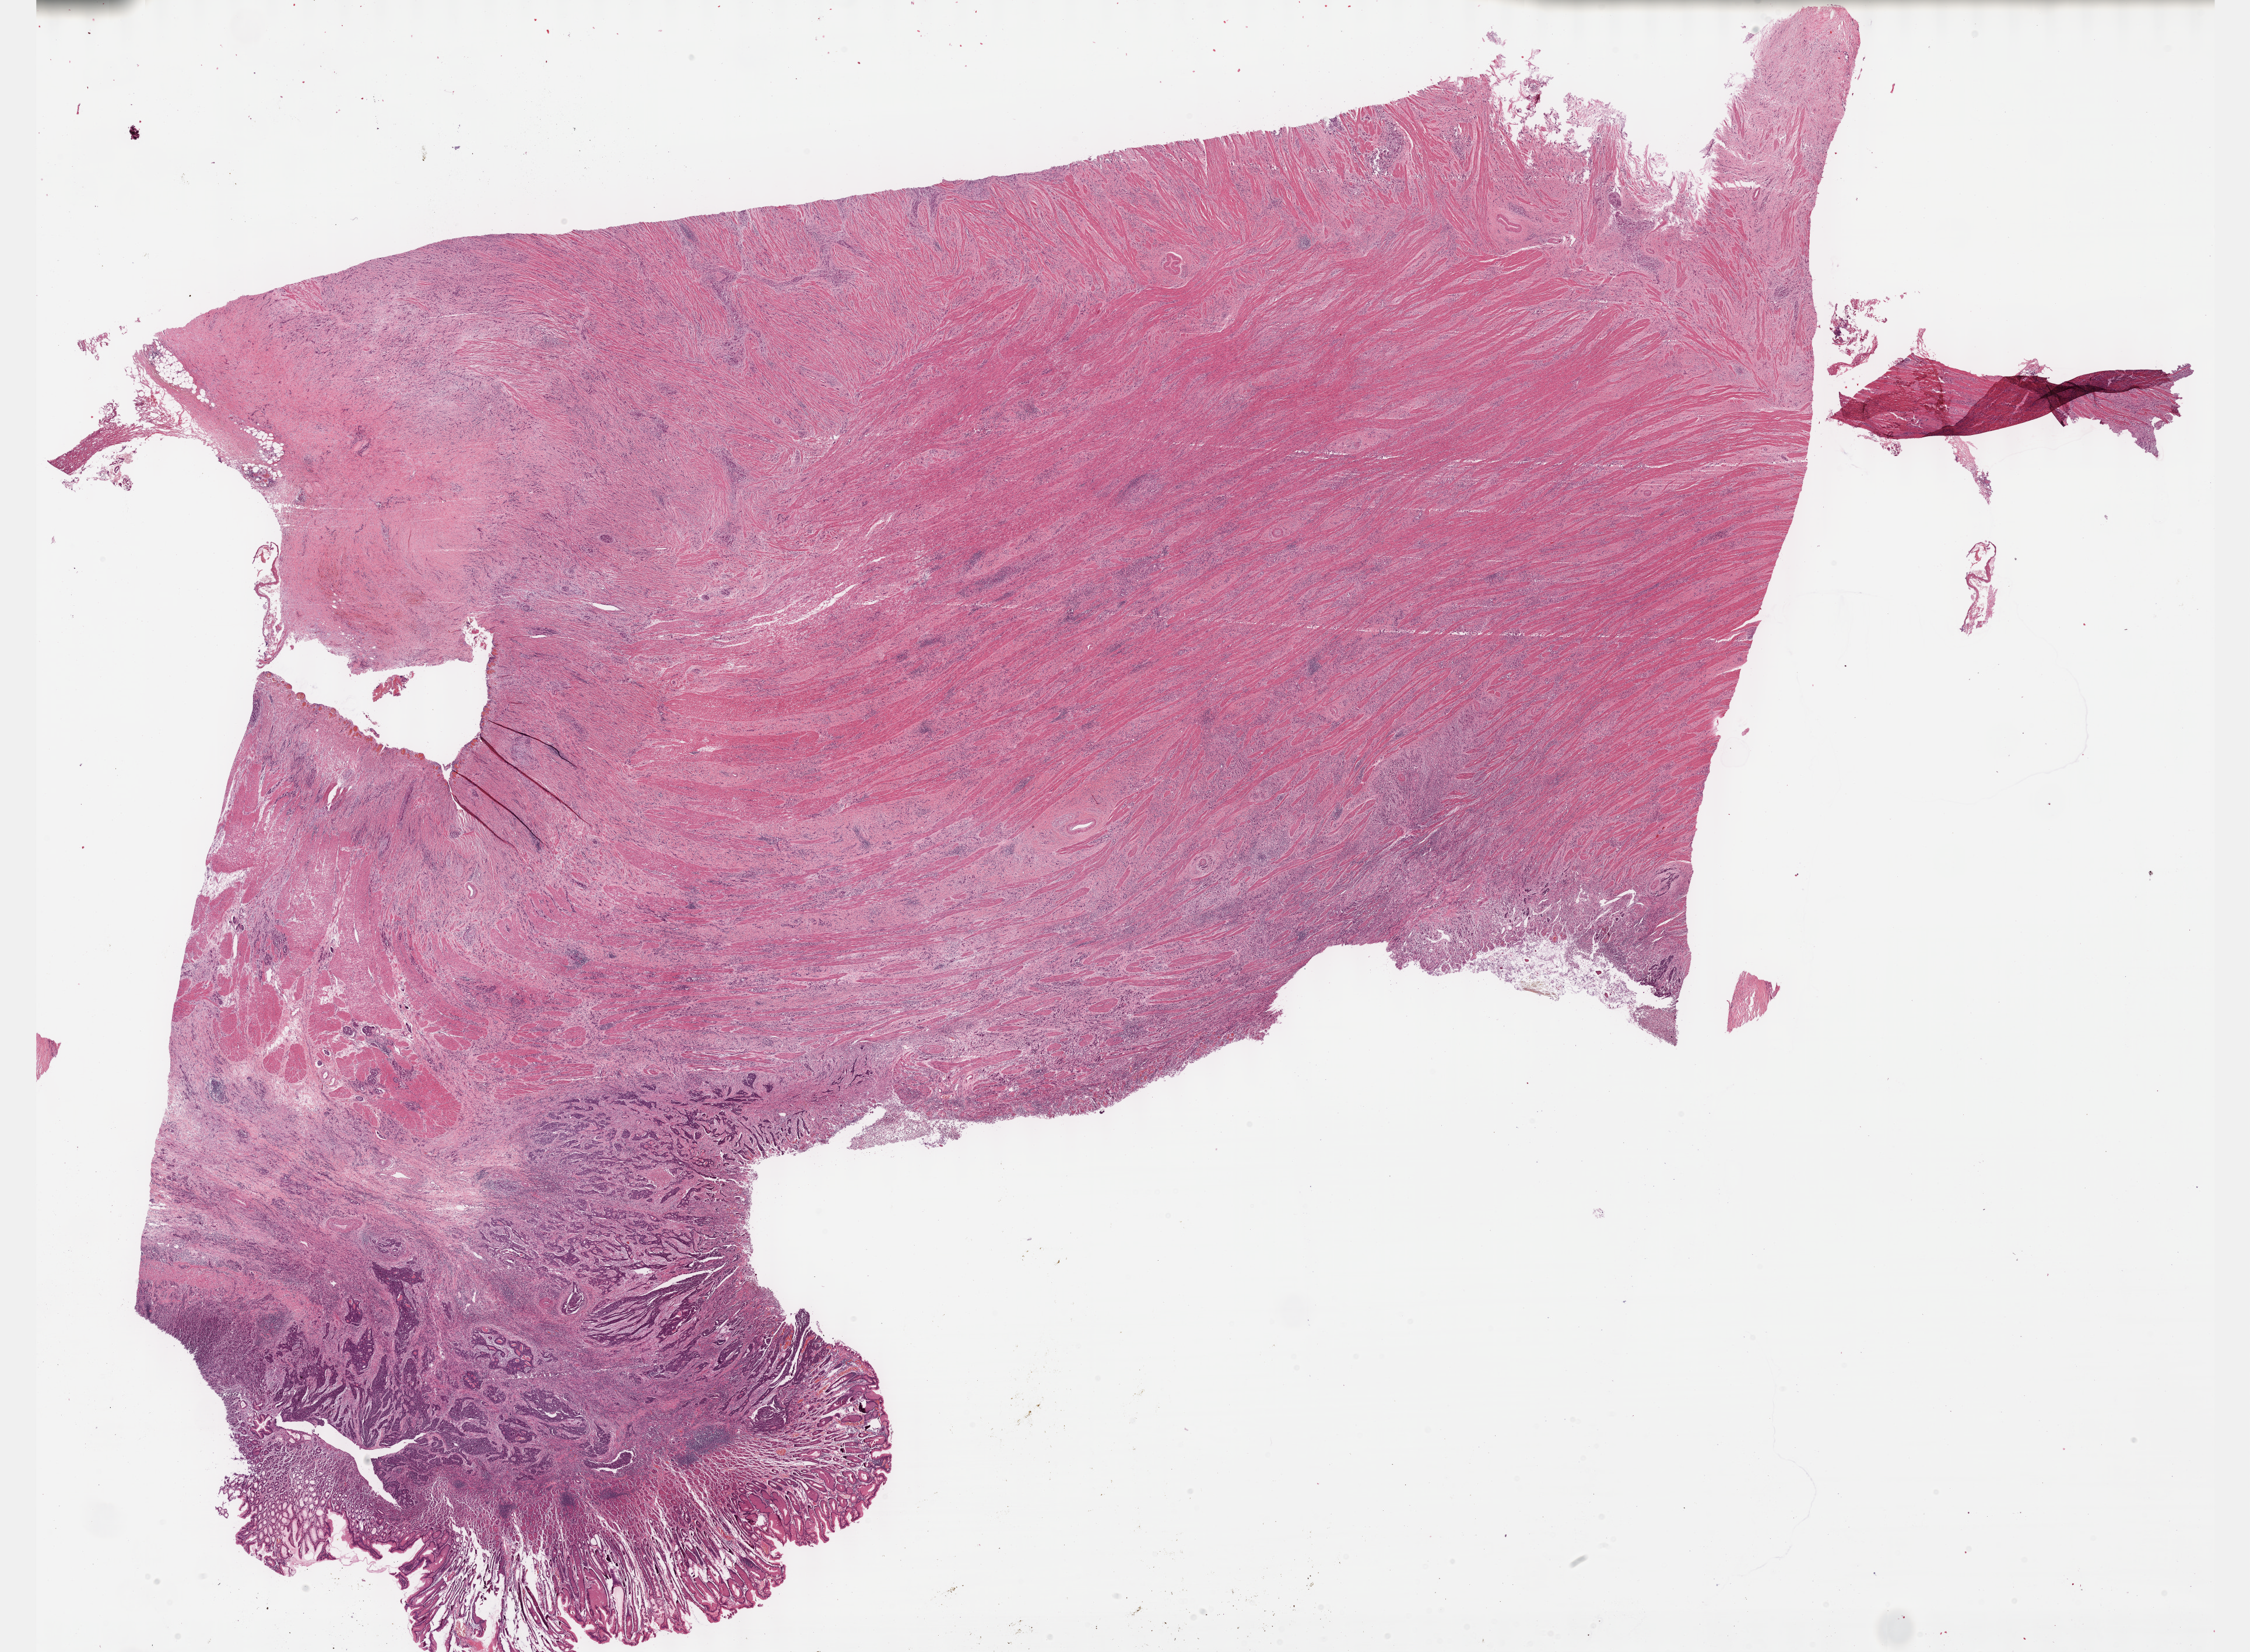
Whole-slide histology image, Hematoxylin and eosin (H&E) stained — whole scanned area (about 31.2 x 22.9 mm, acquisition: 40x scan) shown as a low-resolution overview; formalin-fixed paraffin-embedded (FFPE) diagnostic section; stomach, primary tumour sample. Male, age 62 years at initial diagnosis. Histologic grade: G2 (moderately differentiated).
Histologic diagnosis: Tubular adenocarcinoma (gastric antrum). Lymph nodes positive (case pathology): 24 of 33 examined. AJCC pathologic stage: IIIB (7th edition).